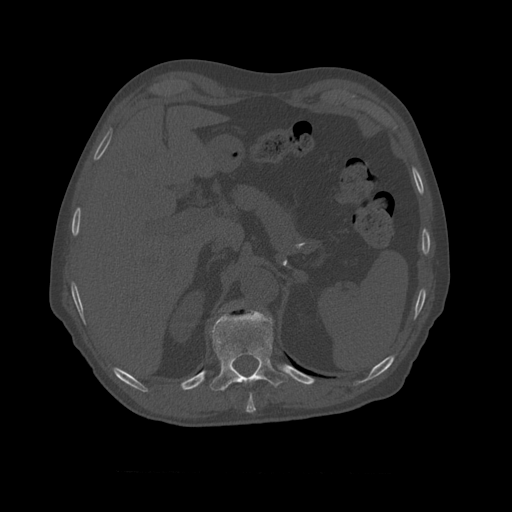
CT including the spine, one axial slice. Slice 402 of 450 in the series (ordered by position). Reconstruction kernel STANDARD. 120 kVp. Bone window (W 1800 / L 400 HU). 1.25 mm slice thickness. 512 × 512 image matrix. Patient age 75 years. From the clinical record (not read from this slice): primary cancer: prostate.
Outlined on this slice (semi-automatic segmentation, software-assisted and operator-edited):
- T10 vertebra: bounding box <209,310,289,392> (left, top, right, bottom; pixels)
- T11 vertebra: <227,302,244,309>
- T9 vertebra: <247,393,256,411>